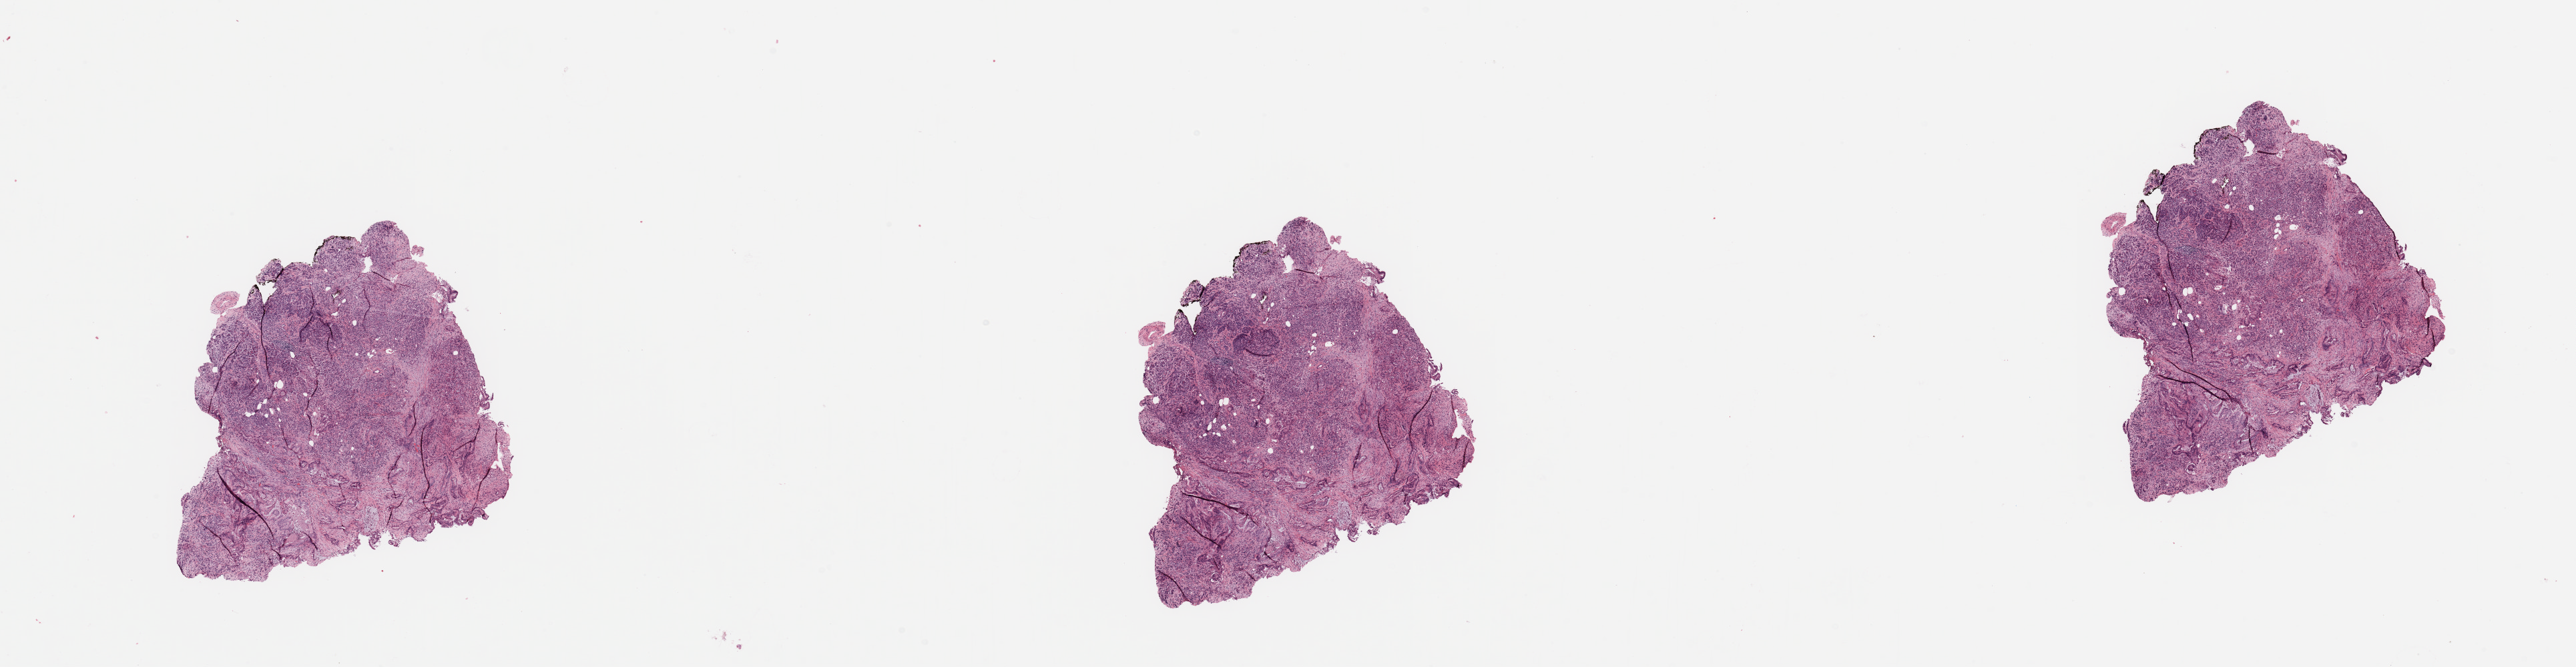
H&E-stained whole-slide image — a low-resolution overview of the entire scanned area, about 30.5 x 7.9 mm. Tumour tissue sample, sampled site: pancreas. Patient: male, age 72 years. Histologic grade: G1 (well differentiated). Composition of this section per pathologist review: tumour nuclei 40%, necrosis 0%.
Diagnosis: Infiltrating duct carcinoma, NOS. AJCC pathologic stage: IIB. Primary tumour site (as recorded): head.